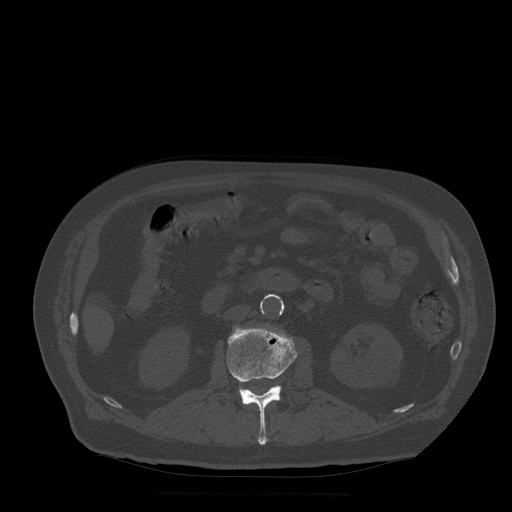
CT including the spine, one axial slice. Position 165 of 522 along the scan axis. Bone window (W 1800 / L 400 HU). 512 × 512 image matrix, field of view 420 × 420 mm. Patient age 72 years. From the clinical record (not read from this slice): primary cancer: prostate.
Annotated regions visible in this slice (semi-automatic segmentation, software-assisted and operator-edited):
- L2 vertebra: bounding box <227,327,297,445> (left, top, right, bottom; pixels)